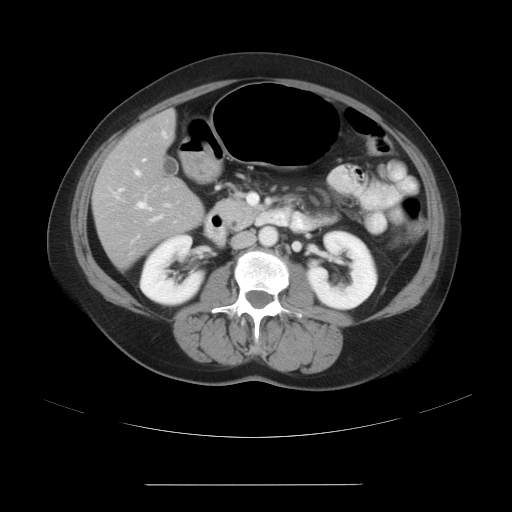
Contrast-enhanced abdominal CT, one axial slice. Slice 11 of 27 in the series (ordered by position). Reconstruction kernel STANDARD. 120 kVp. Soft-tissue window (W 400 / L 40 HU). 7.5 mm slice thickness. 512 × 512 image matrix, field of view 440 × 440 mm. Female patient, age 58 years. From the clinical record (not read from this slice): diagnosis: colorectal cancer liver metastases, imaged before liver resection; multiple liver metastases: yes; largest metastasis: 1.9 cm.
Annotated regions visible in this slice (manually delineated by an expert):
- hepatic veins: box from (x=137, y=202) to (x=152, y=211) px
- liver: (x=93, y=113)–(x=202, y=268)
- planned liver remnant (the part of the liver to remain after resection): (x=98, y=112)–(x=195, y=203)
- portal vein (with intrahepatic branches): (x=113, y=131)–(x=171, y=244)